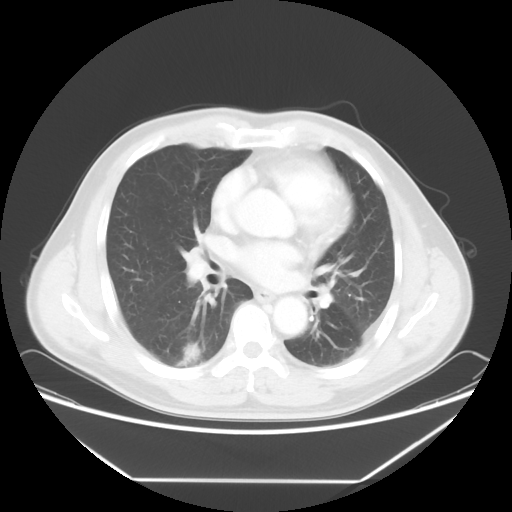
Chest CT, one axial slice. Position 35 of 65 along the scan axis. Reconstruction kernel STANDARD. 120 kVp. Lung window (W 1500 / L -600 HU). 5 mm slice thickness. 512 × 512 image matrix, field of view 418 × 418 mm. Male patient, age 50 years. Case-level facts recorded for this patient, not image findings: clinical TNM (as recorded): T1c N0 M0; histopathological grade: G3.
Structures marked on this image (rectangle marked by the reading radiologist):
- lung tumour (recorded histology: adenocarcinoma): box from (x=172, y=341) to (x=203, y=368) px